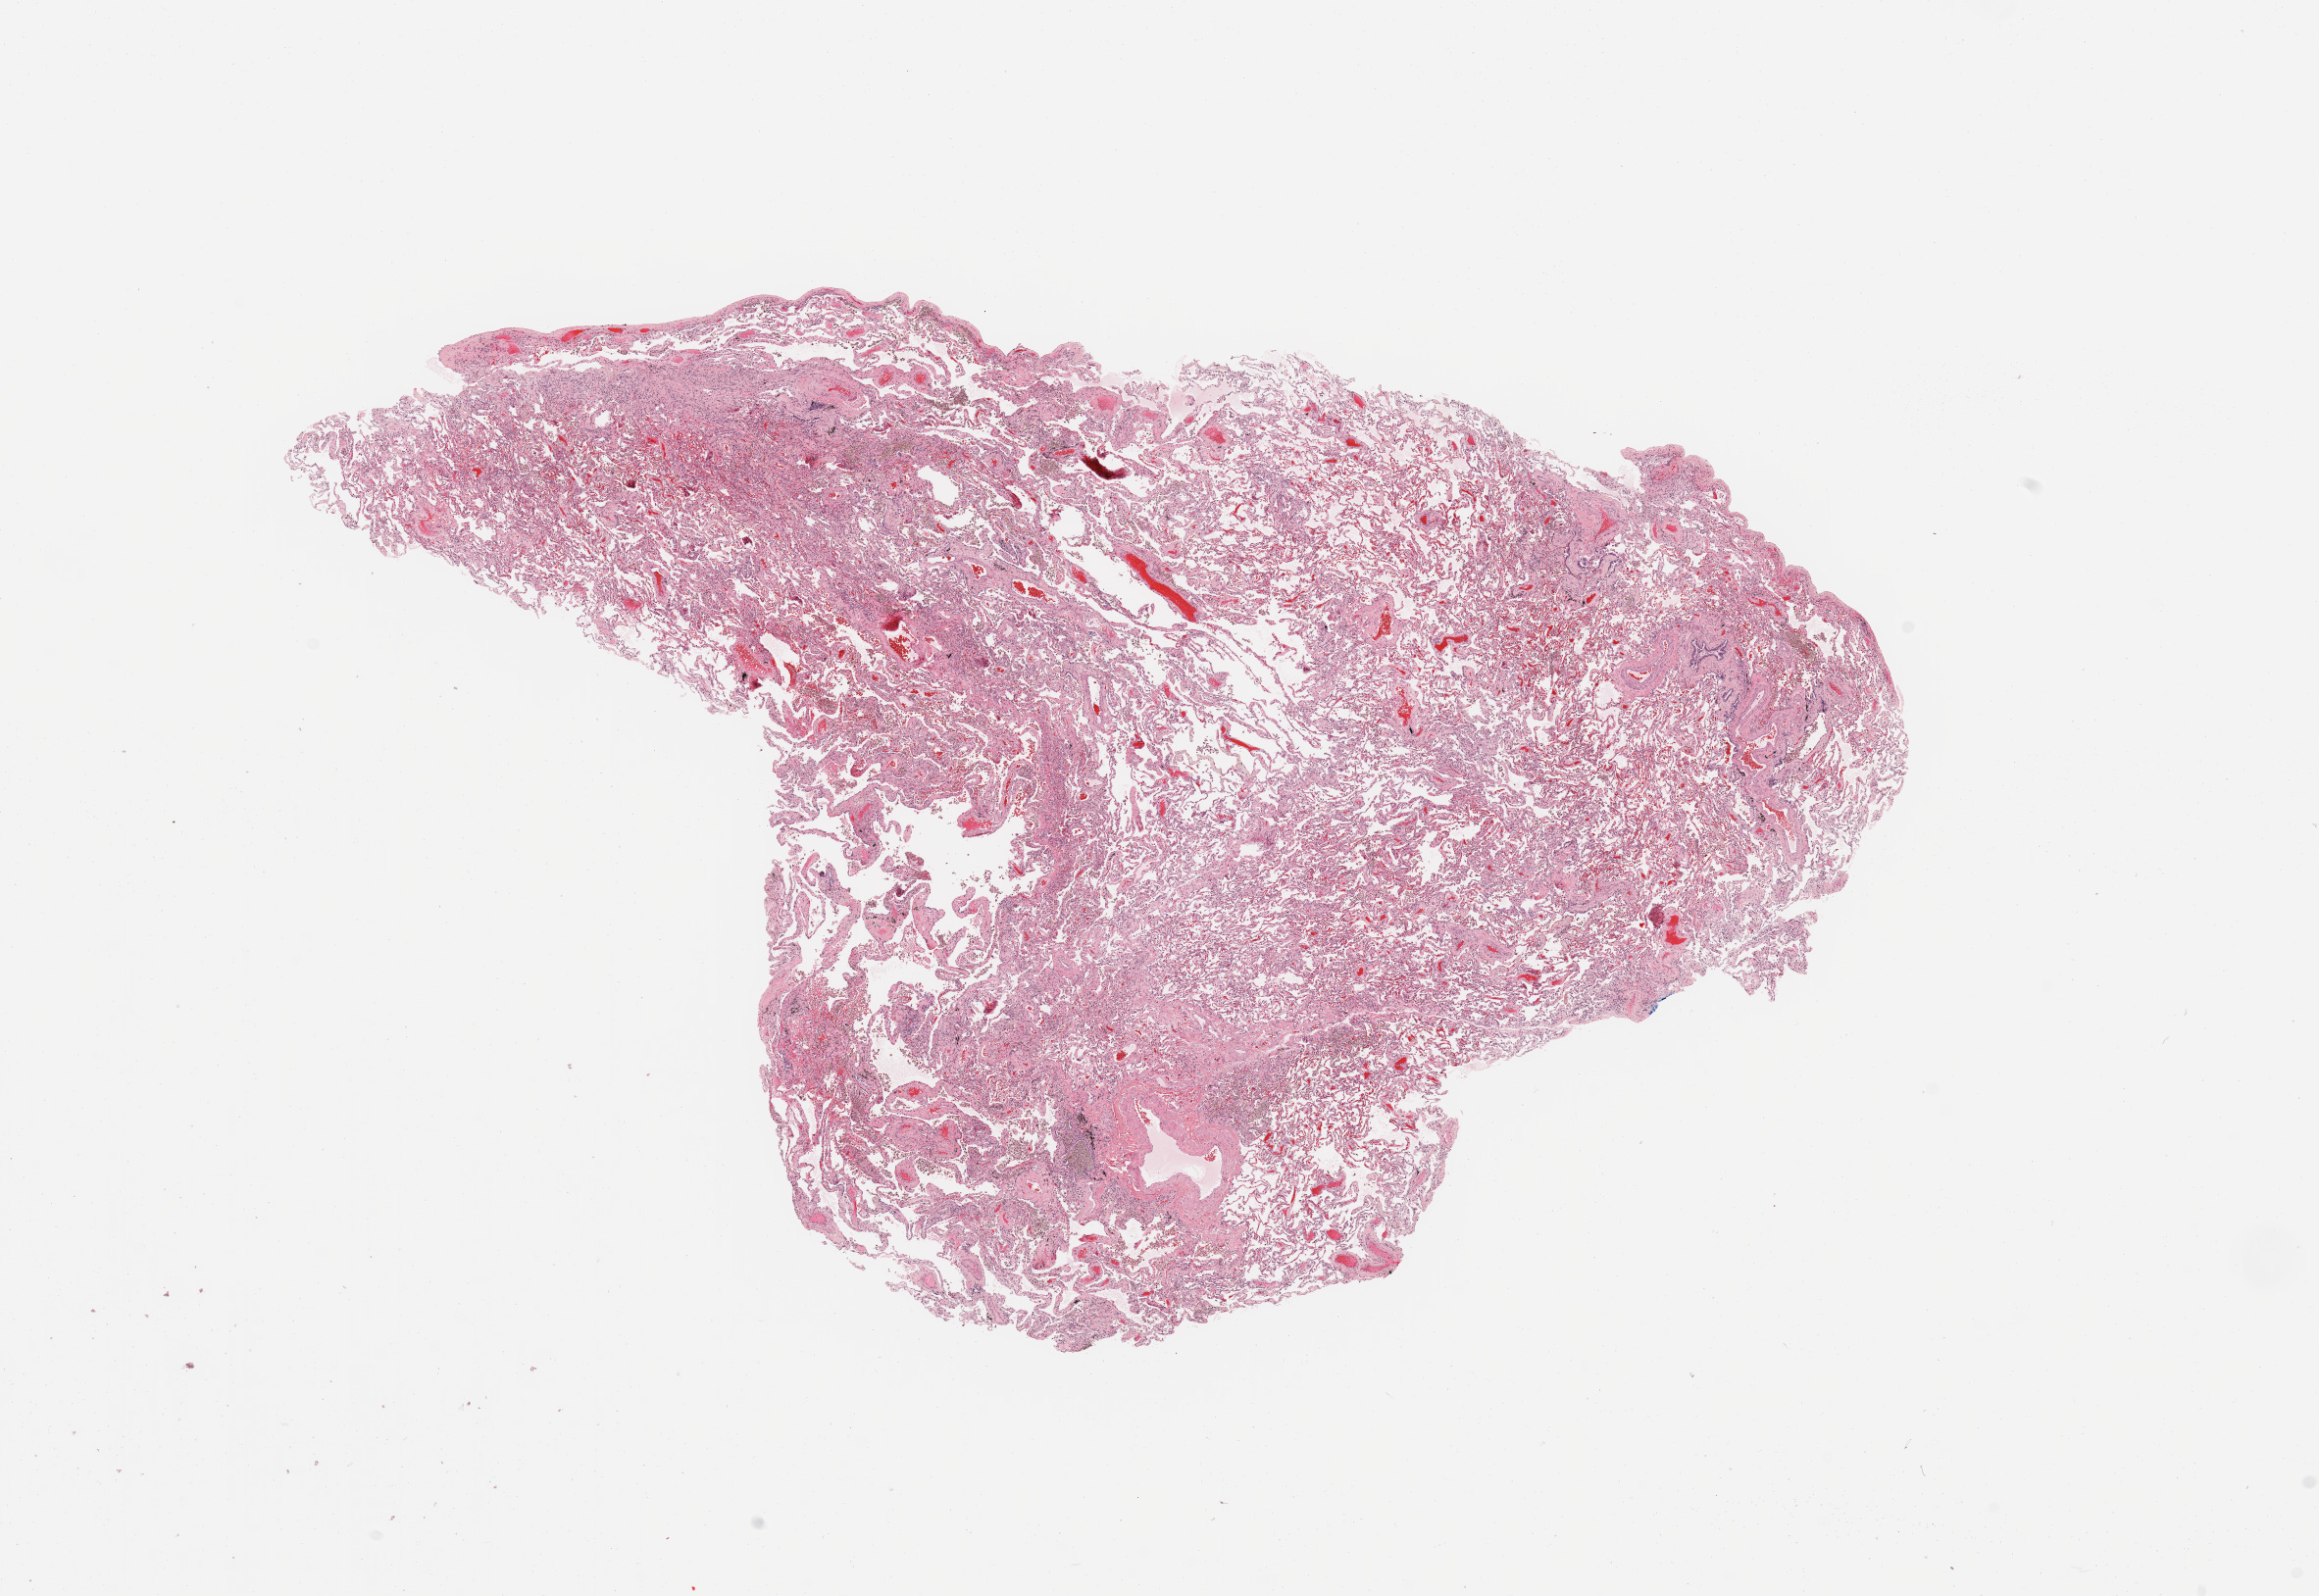
H&E-stained whole-slide image — whole scanned area (about 18.7 x 12.9 mm, from a 20x scan) shown as a low-resolution overview; normal (non-tumour) tissue sample, sampled site: lung. Female, 52 y/o.
* this section: normal (non-tumour) tissue from the same patient
* patient diagnosis: Adenocarcinoma, NOS